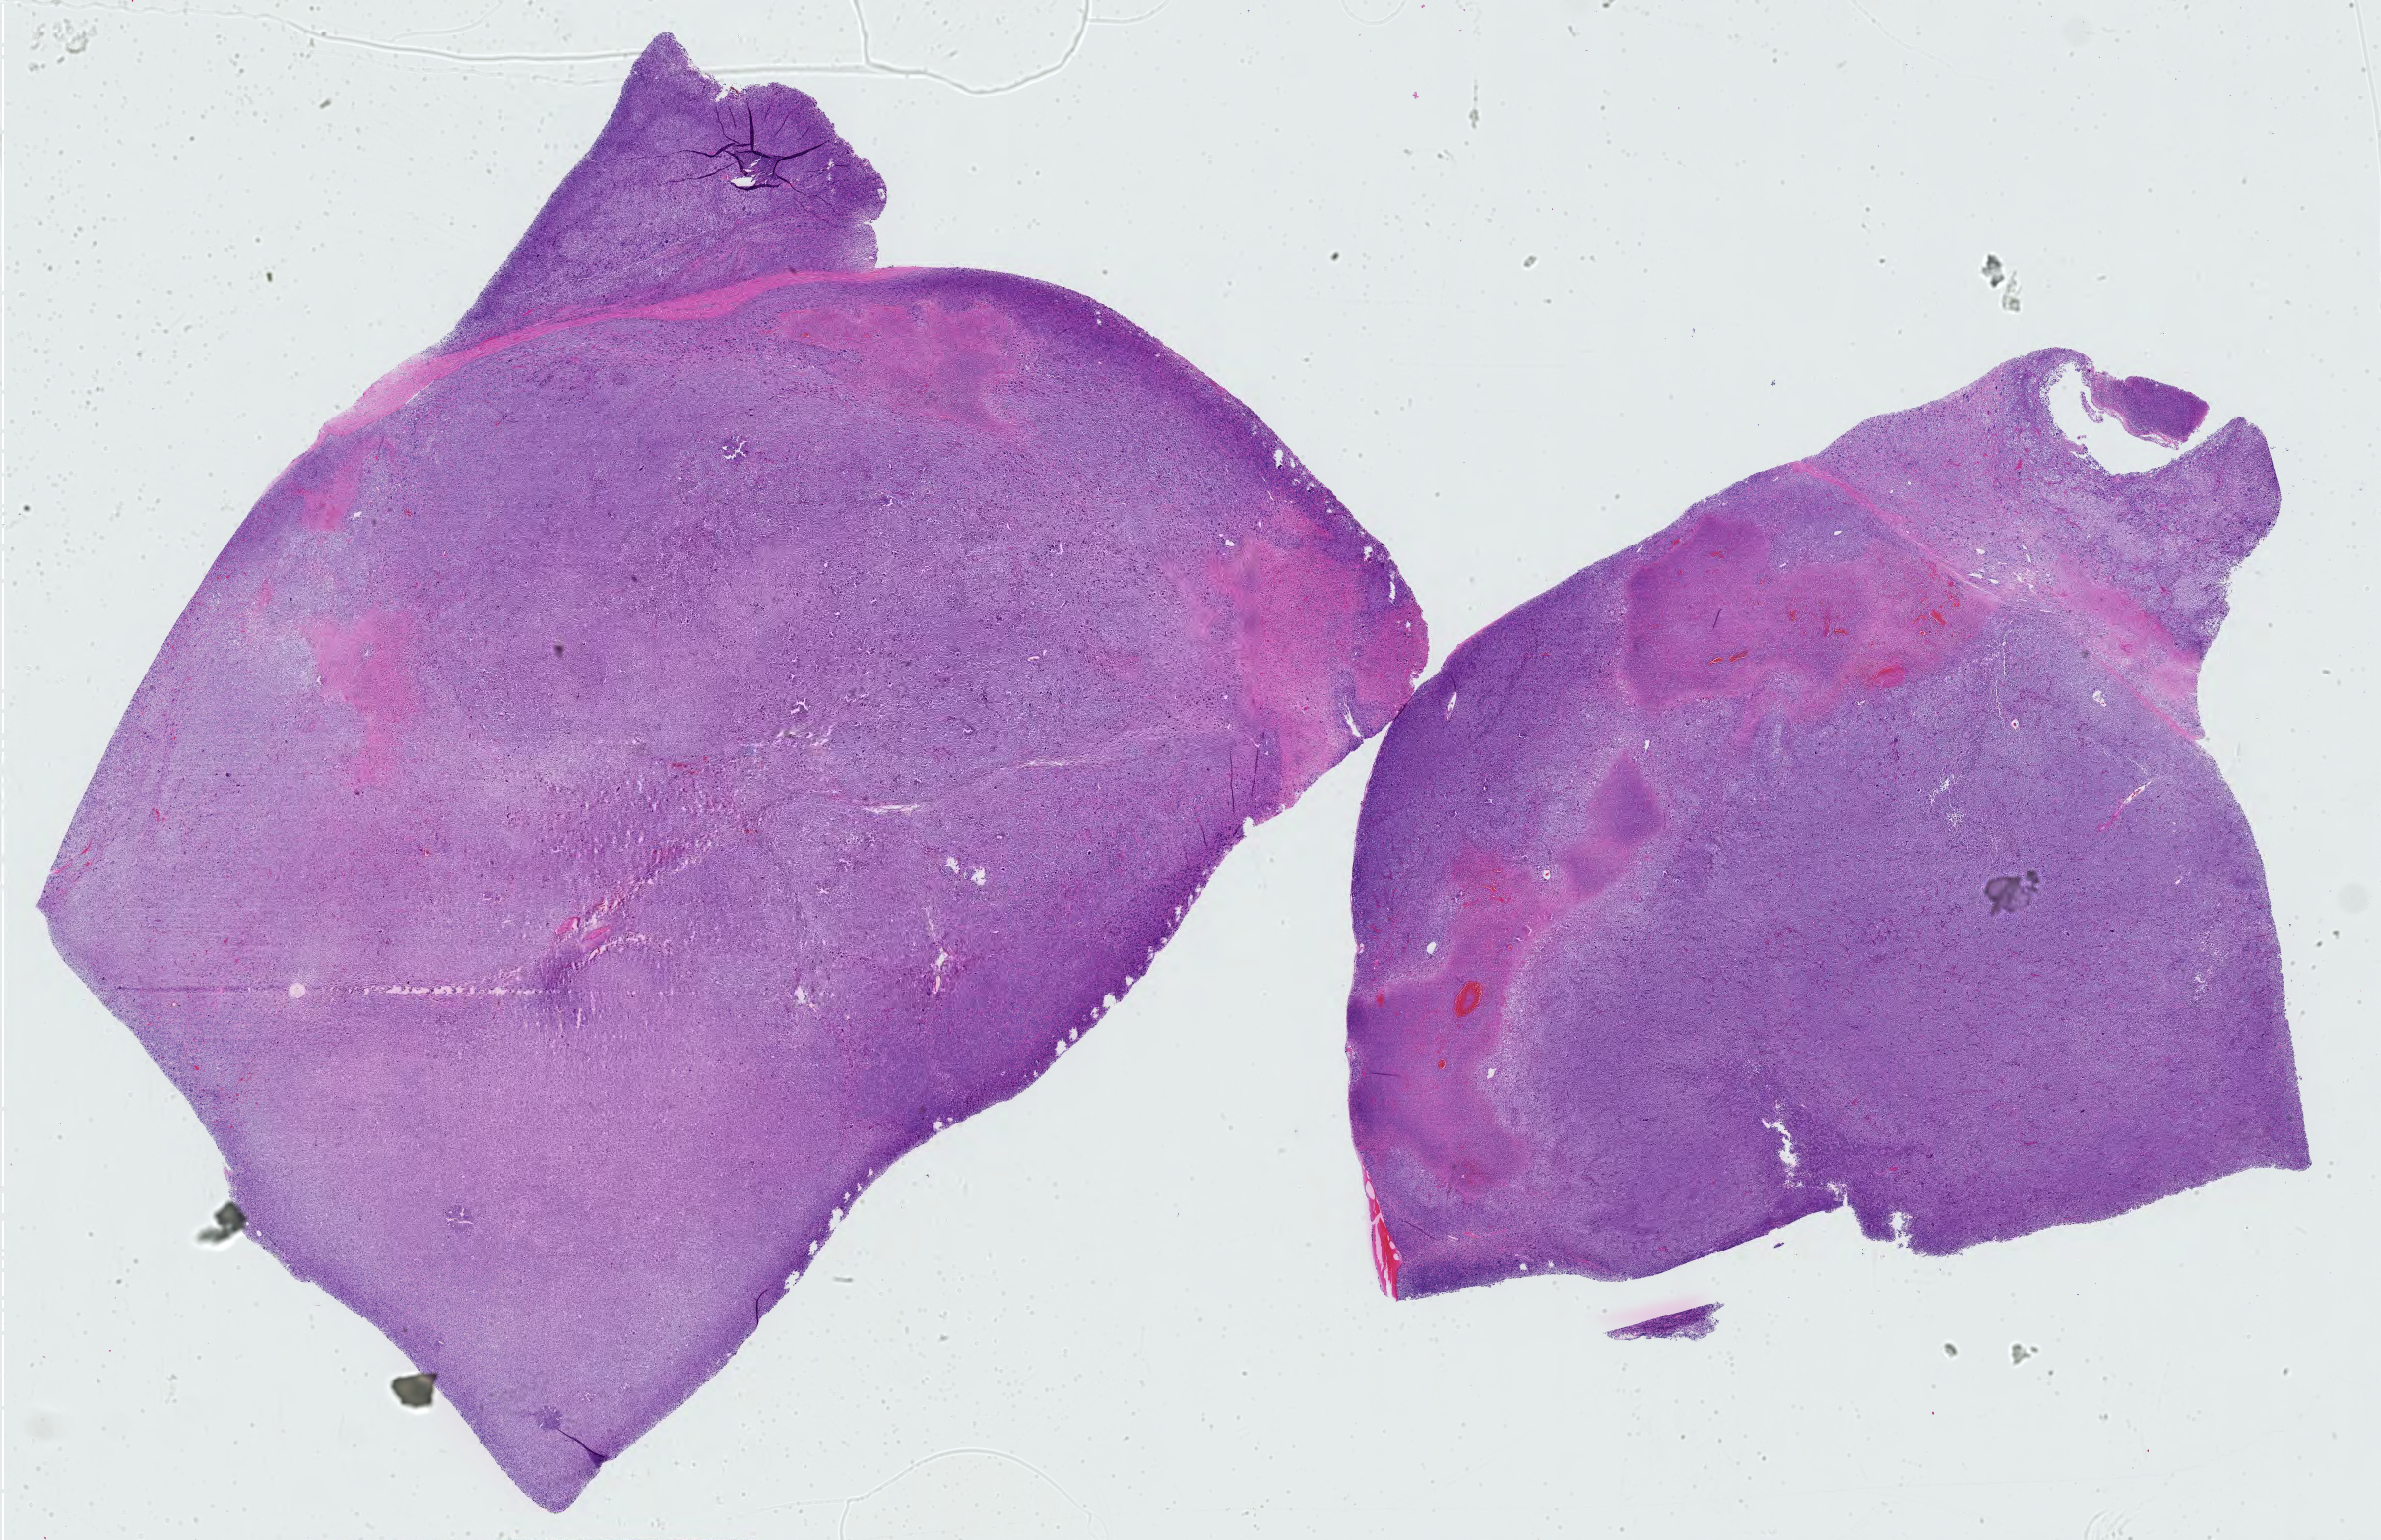
Digitized H&E-stained tissue section (whole slide) — shown as a low-resolution overview of the whole scanned area (about 35.1 x 22.7 mm, from a 40x scan). Formalin-fixed paraffin-embedded (FFPE) diagnostic section. Primary tumour sample from the connective, subcutaneous and other soft tissues. Patient: female, age at initial diagnosis 53 years.
Histologic diagnosis: Undifferentiated sarcoma (connective, subcutaneous and other soft tissues of pelvis).